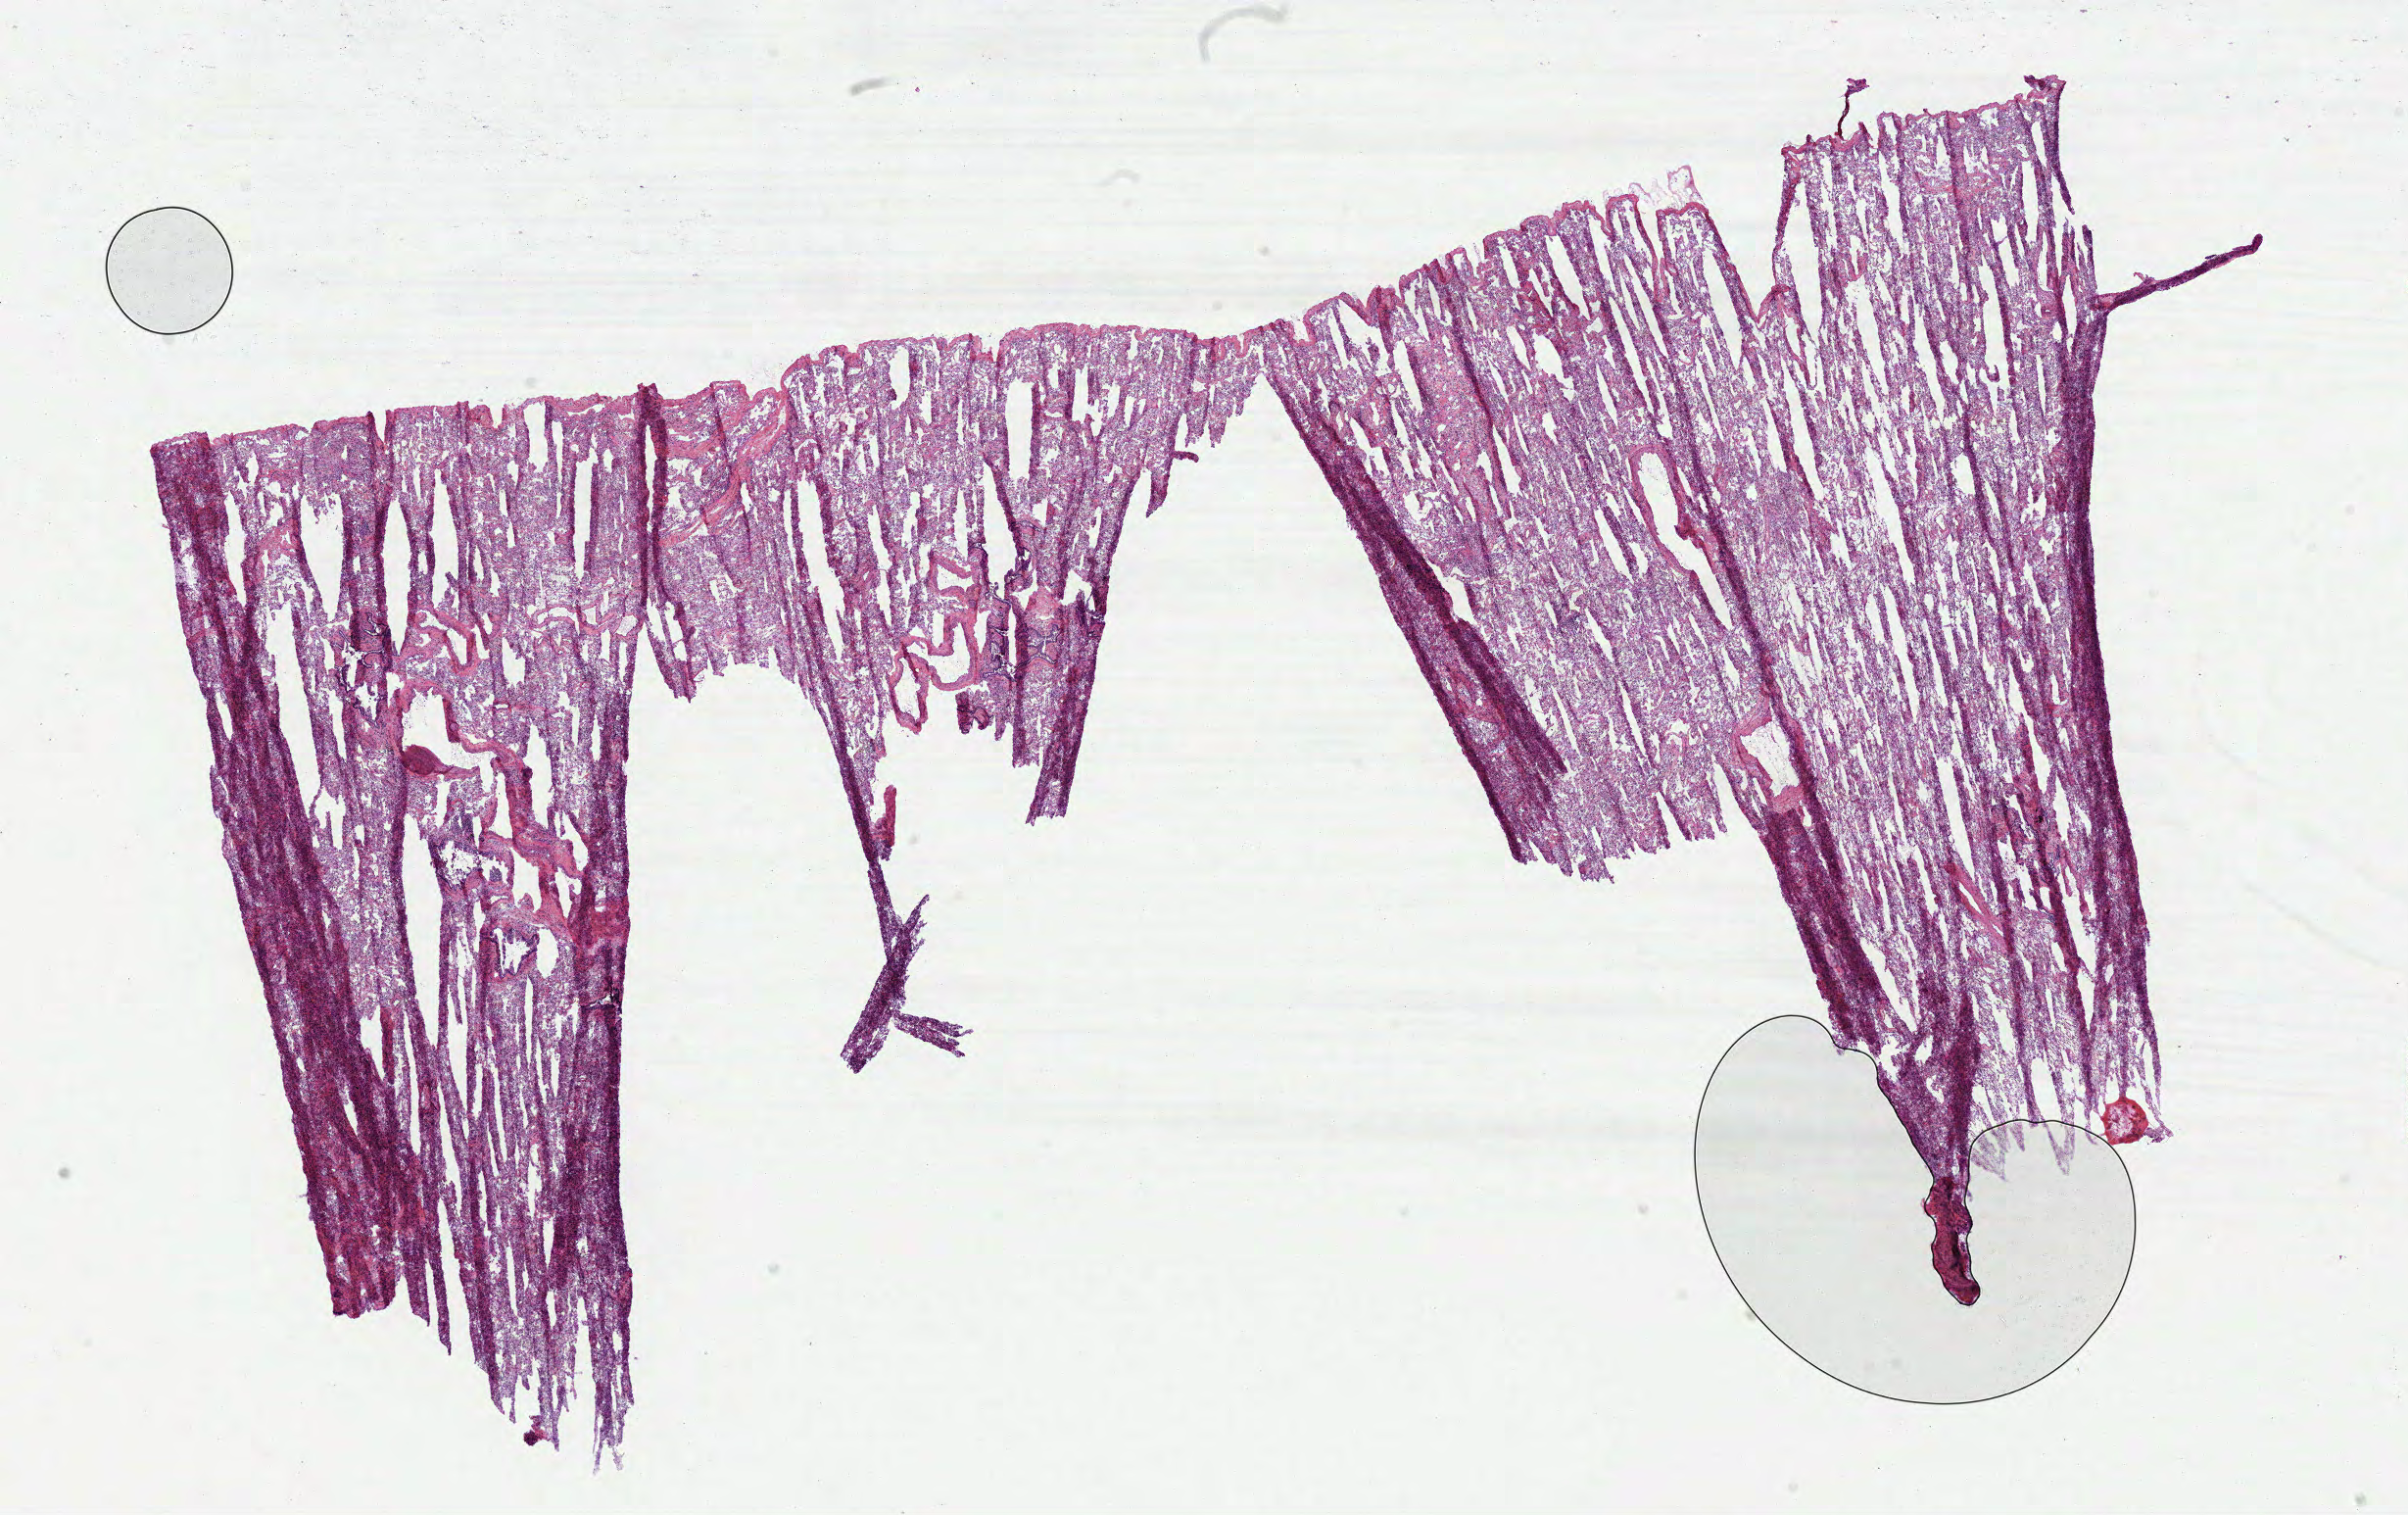
Digitized H&E-stained tissue section (whole slide) — whole scanned area (about 19.8 x 12.5 mm) shown as a low-resolution overview. Frozen section. Lung, solid tissue normal (non-tumour tissue) sample. Patient: female, age at initial diagnosis 68 years.
* this section: solid tissue normal sample (biorepository sample class)
* patient diagnosis: Bronchiolo-alveolar adenocarcinoma, NOS (lower lobe, lung)